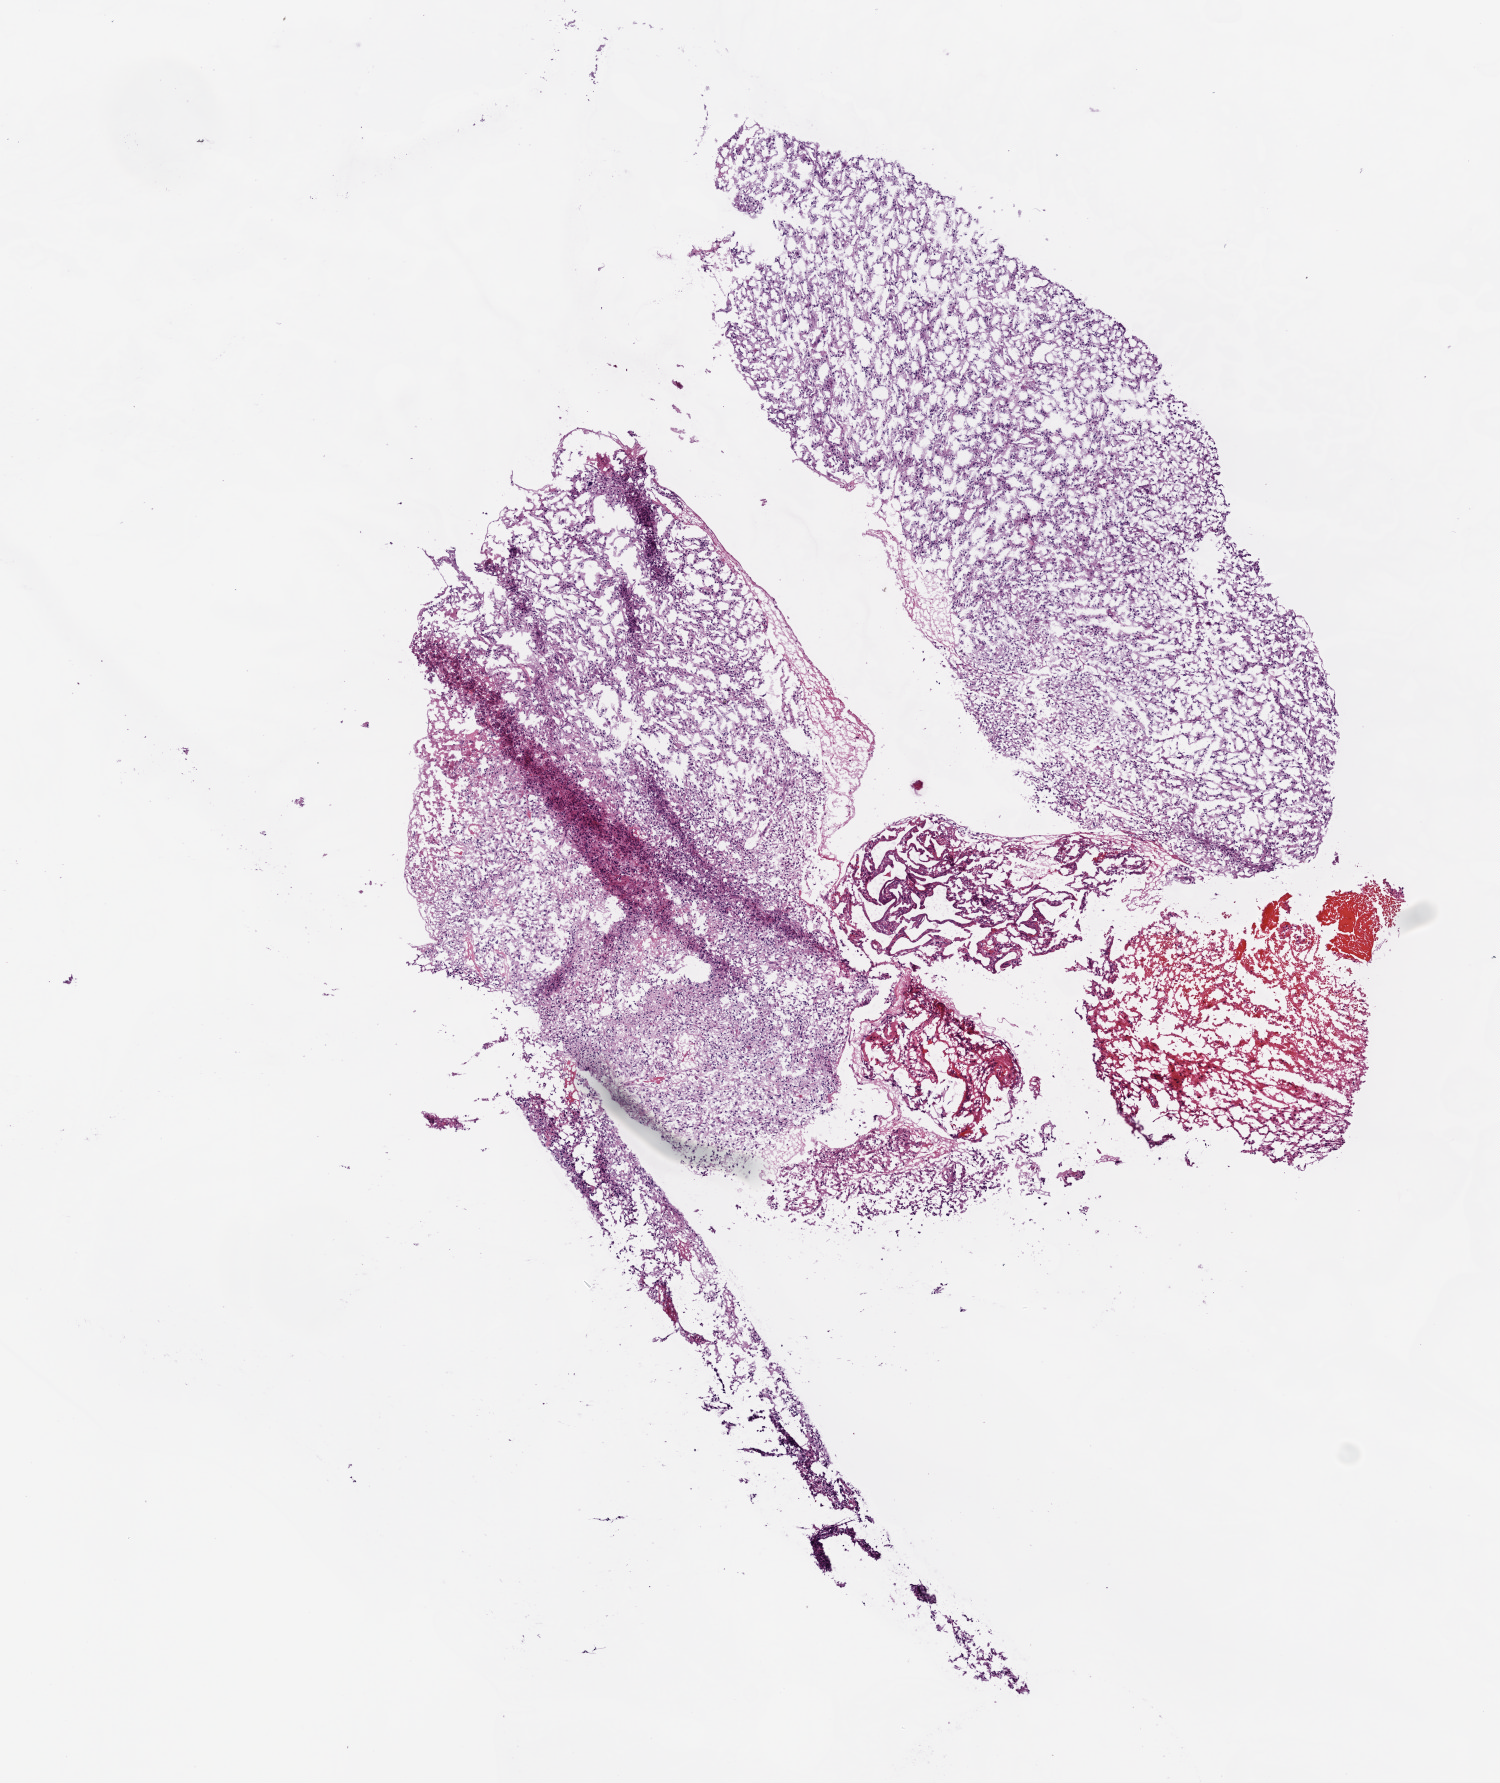
Whole-slide histology image, H&E-stained, low-resolution overview of the scanned area, about 6.0 x 7.2 mm (from a 20x scan); frozen section from the bottom of the tissue portion; sample: primary tumour, brain. Patient: female, age at initial diagnosis 59 years. Composition of this section per pathologist review: tumour cells 75%, tumour nuclei 85%, normal cells 0%, stromal cells 10%, necrosis 15%.
Pathologic diagnosis: Glioblastoma.